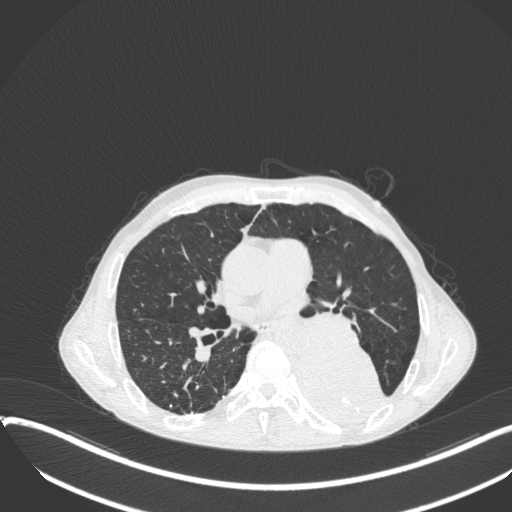
Chest CT, one axial slice; lung window (W 1500 / L -600 HU); 1 mm slice thickness; 512 × 512 image matrix. Patient: male, 57 years. Case-level facts recorded for this patient, not image findings: clinical TNM (as recorded): T4 N0 M0.
Annotated regions visible in this slice (bounding box drawn by a radiologist):
- lung tumour (recorded histology: squamous cell carcinoma): box from (x=282, y=341) to (x=387, y=427) px